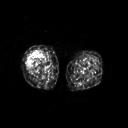
FDG PET of an extremity soft-tissue mass (from a PET/CT study), one axial slice; position 219 of 311 along the scan axis; 3.27 mm slice thickness; 128 × 128 image matrix, field of view 500 × 500 mm. Female patient, age 57 years. From the clinical record (not read from this slice): histological type: pleiomorphic undifferentiated sarcoma; grade: high; site of the primary tumour: right quadricep.
Annotated regions visible in this slice (expert contour drawn on MRI and transferred to this co-registered scan by the dataset authors):
- tumour plus oedema (research contour): box from (x=26, y=51) to (x=41, y=68) px